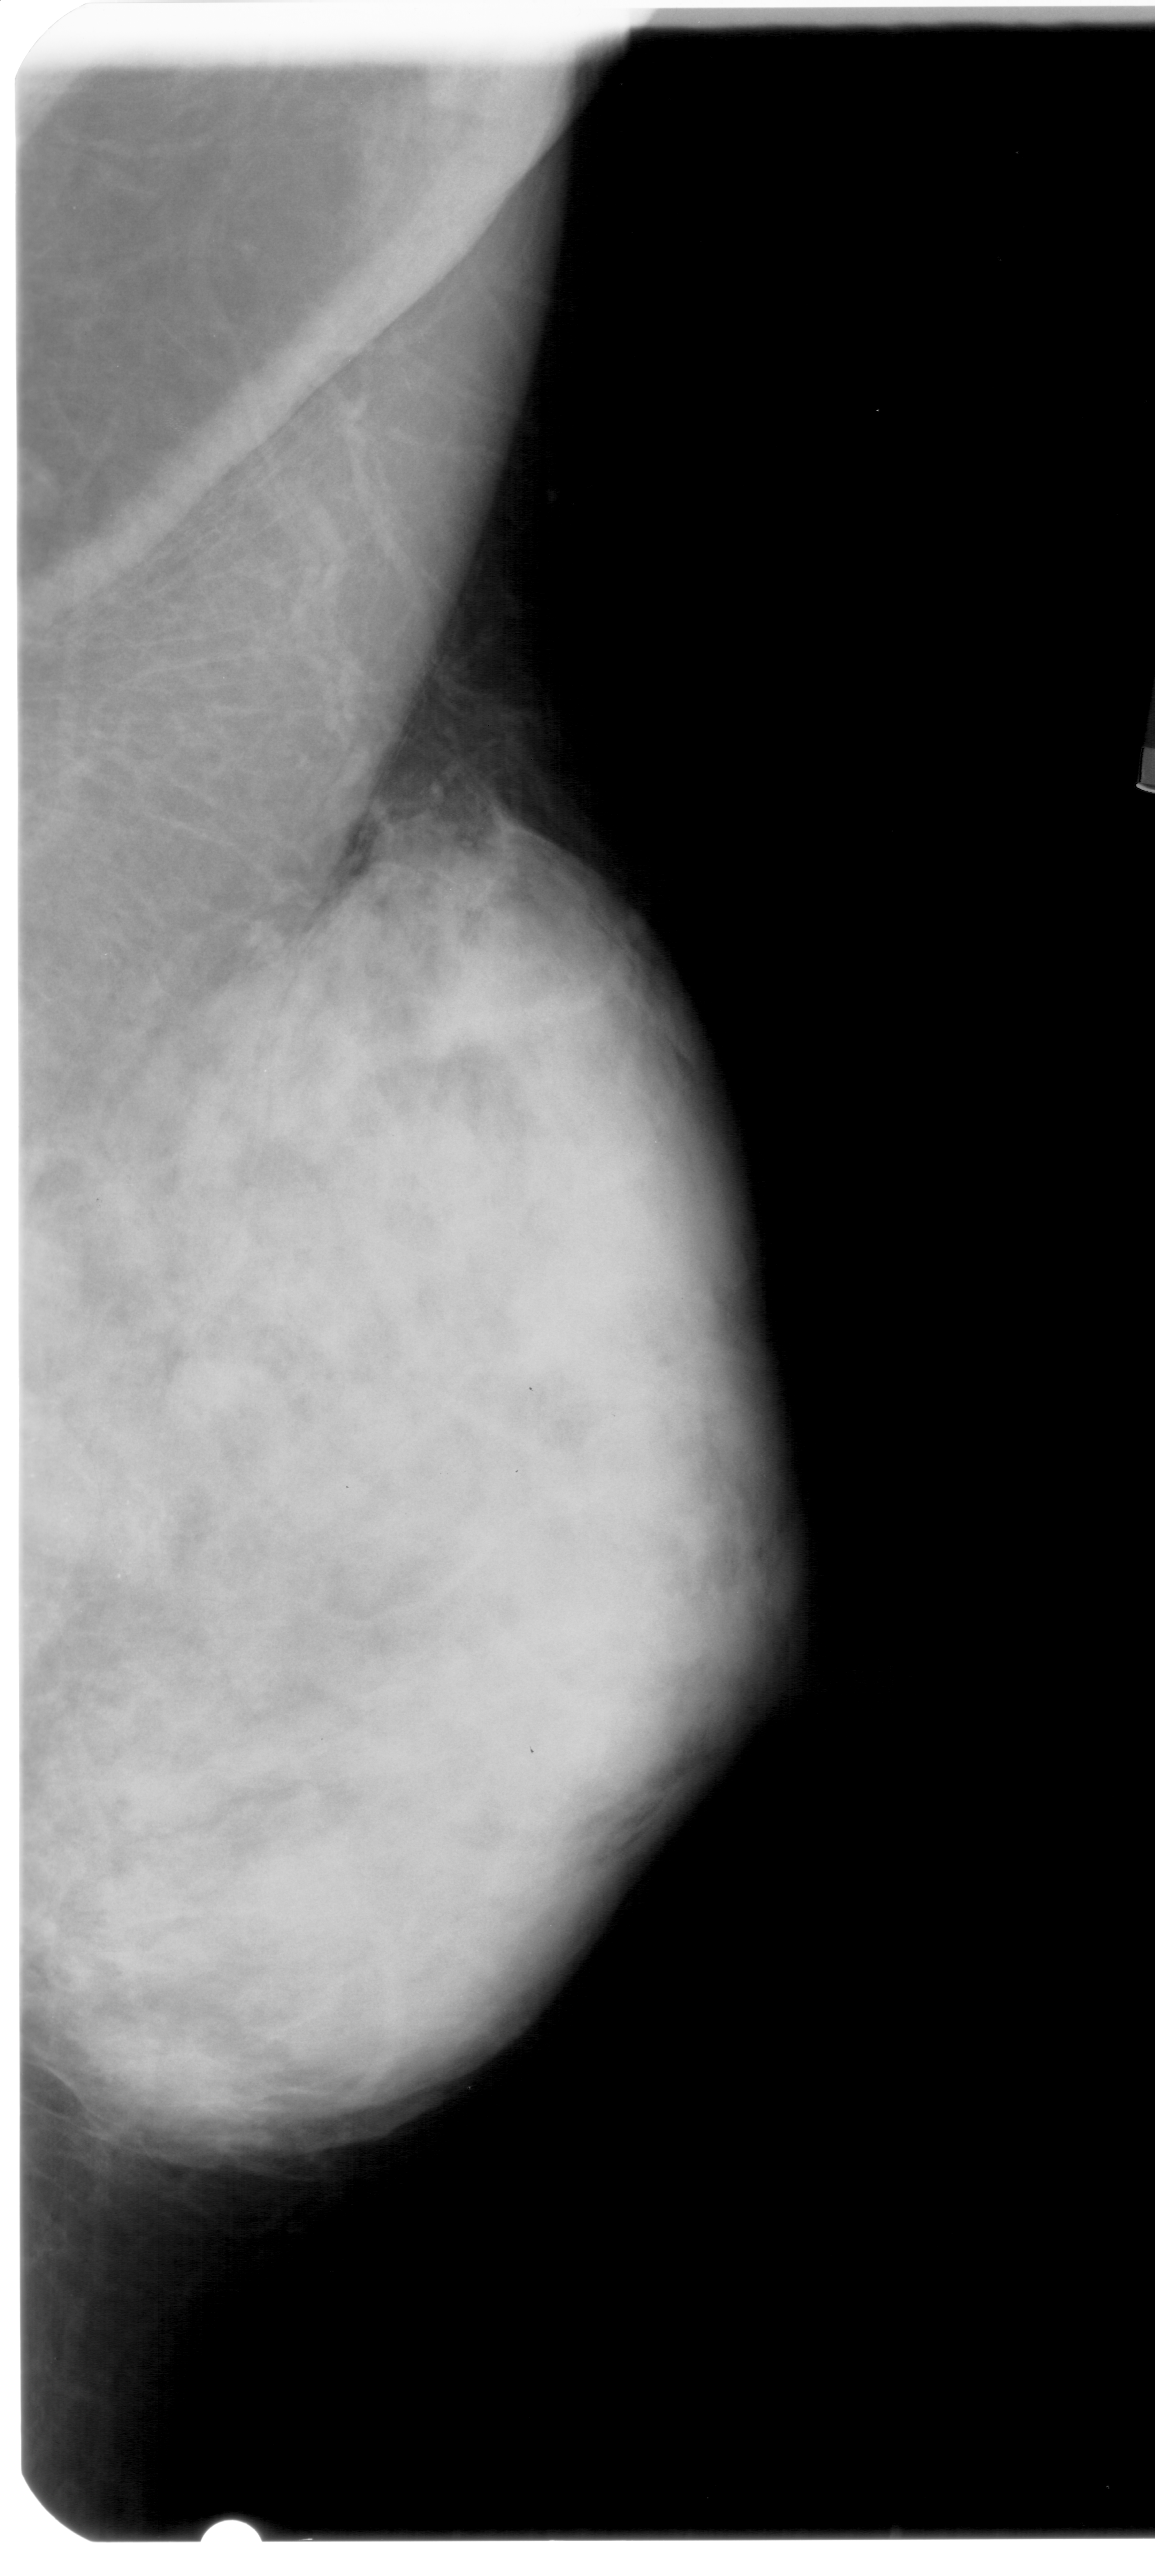
Mammogram (digitized film); right breast; mediolateral oblique (MLO) view; BI-RADS breast density category 4 (scale 1–4).
- Radiologist-marked abnormalities on this image: calcifications, morphology pleomorphic, distribution clustered; BI-RADS assessment category 4; pathology result (as recorded, not read from the image): benign.